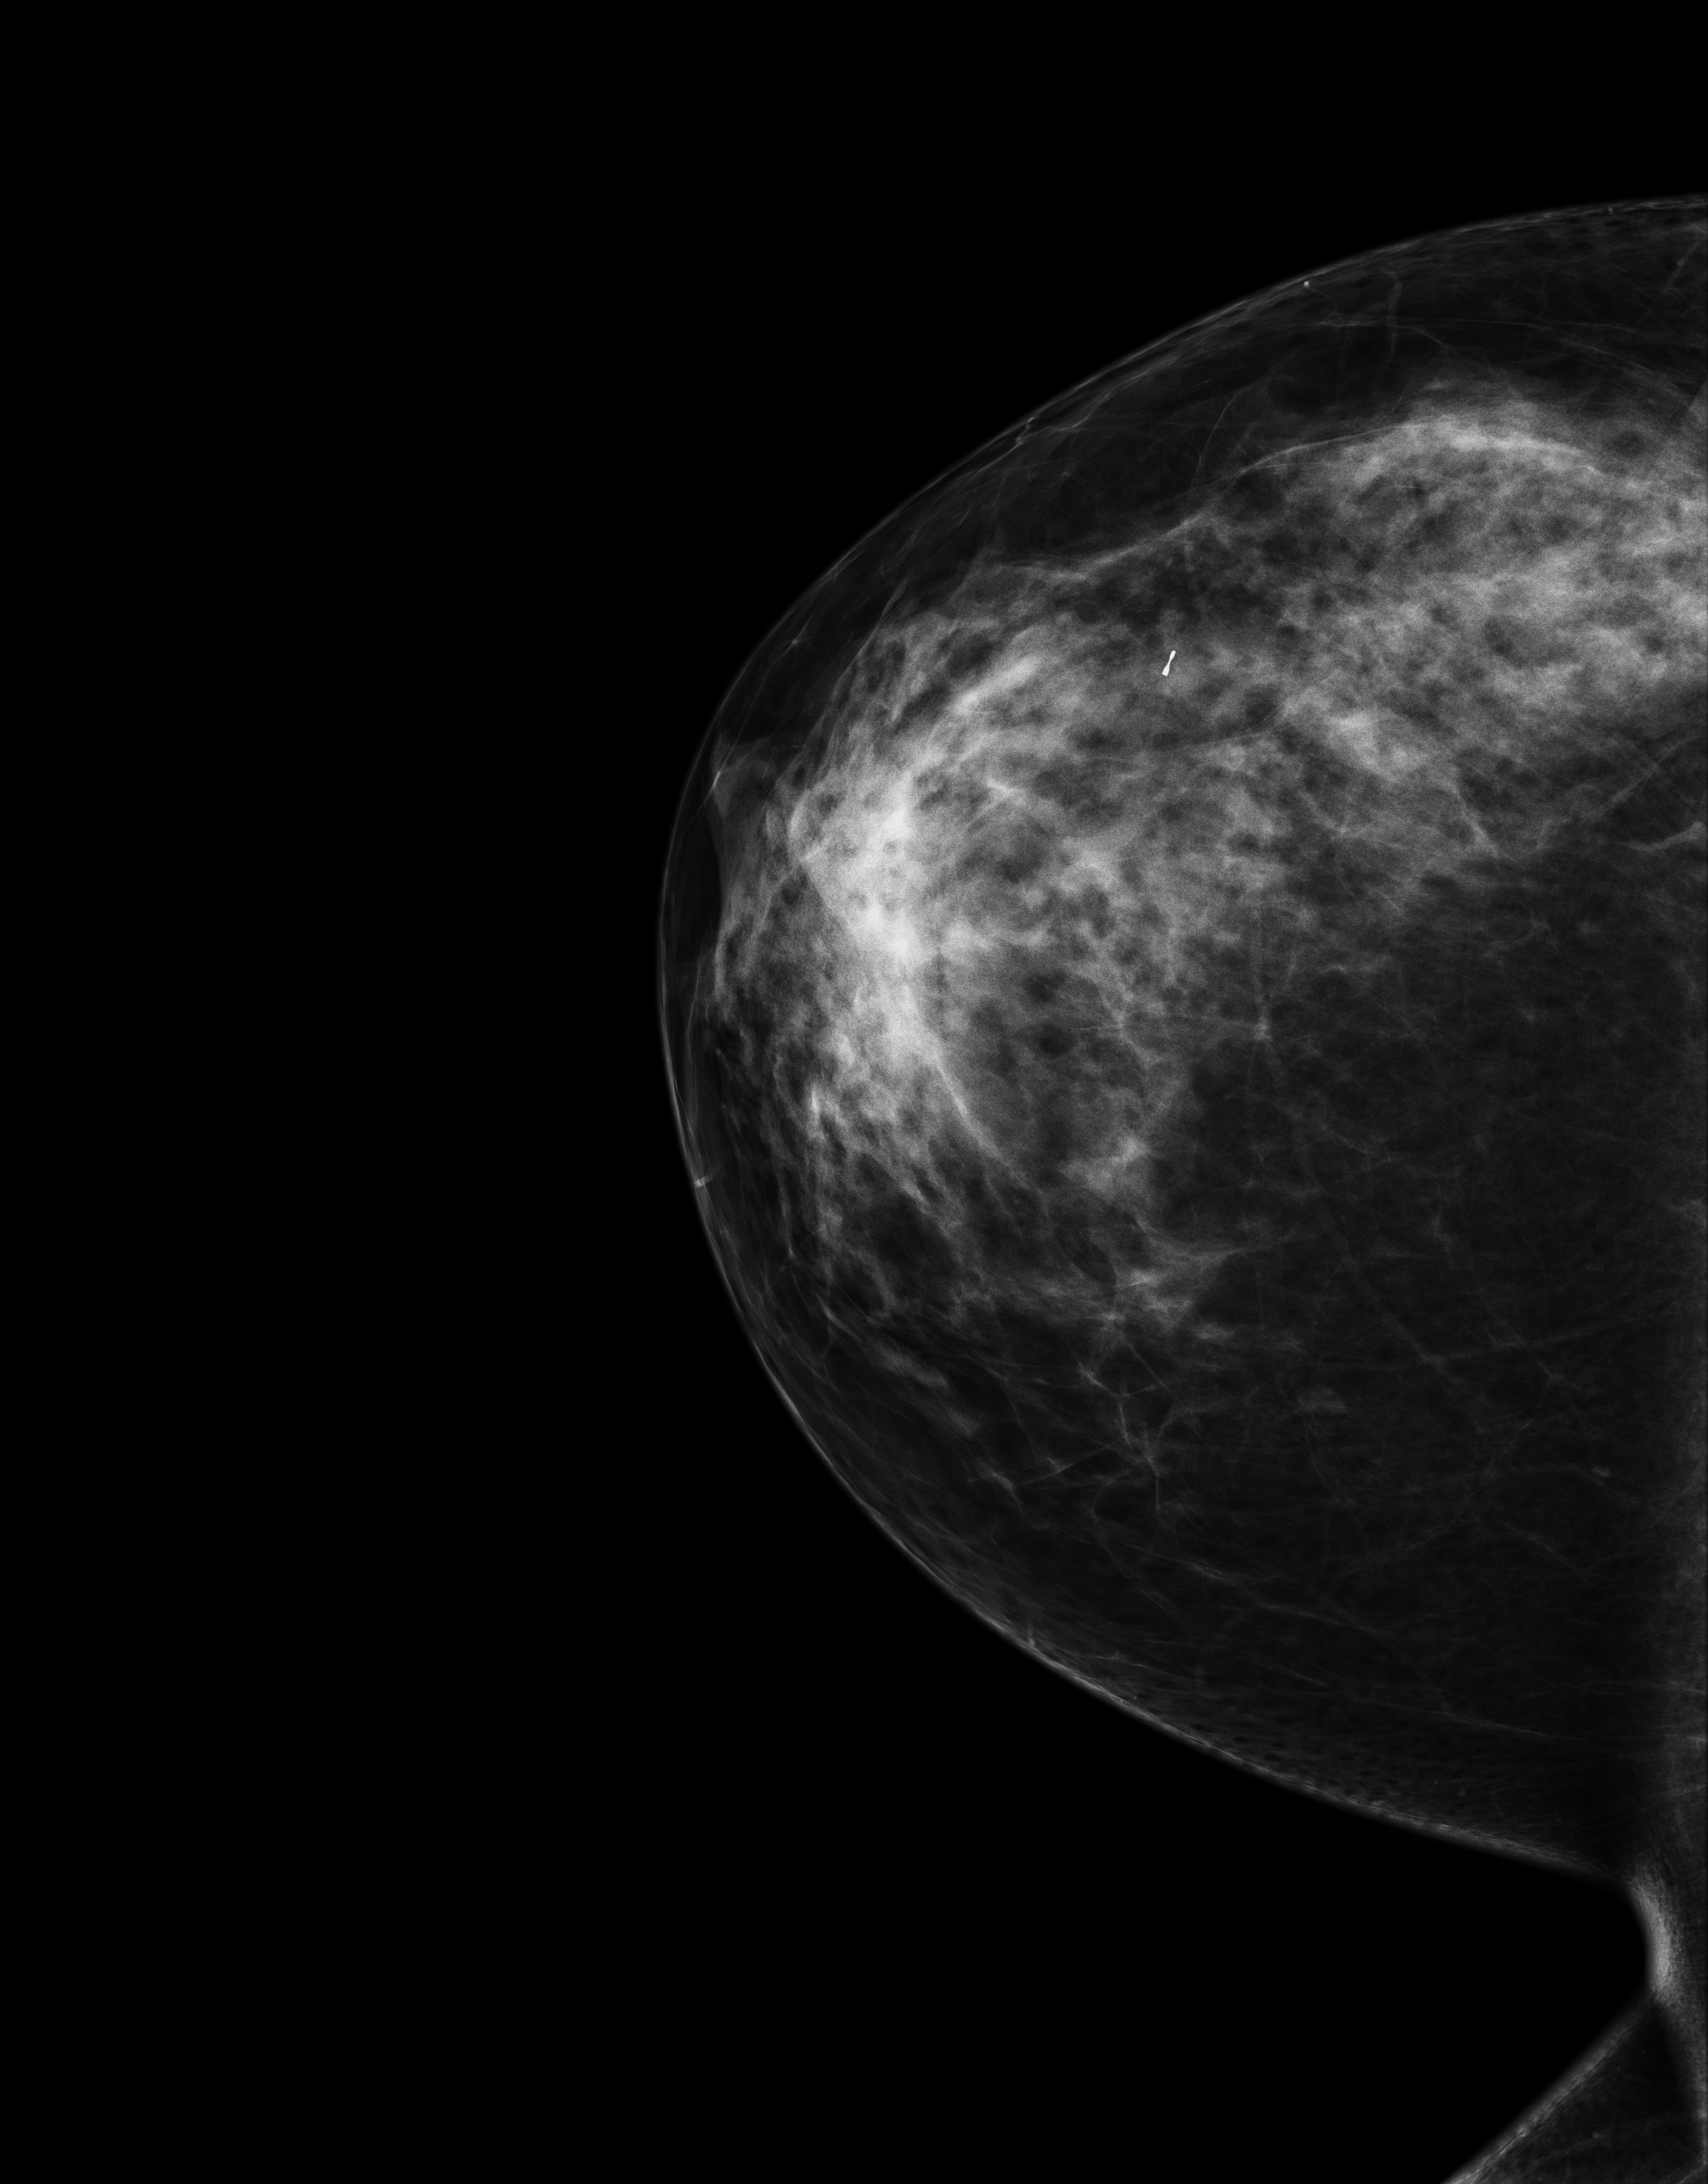
Screening examination. Patient aged 43 years (female).
Image type: full-field digital mammogram. Breast: right. Projection: cranio-caudal projection.